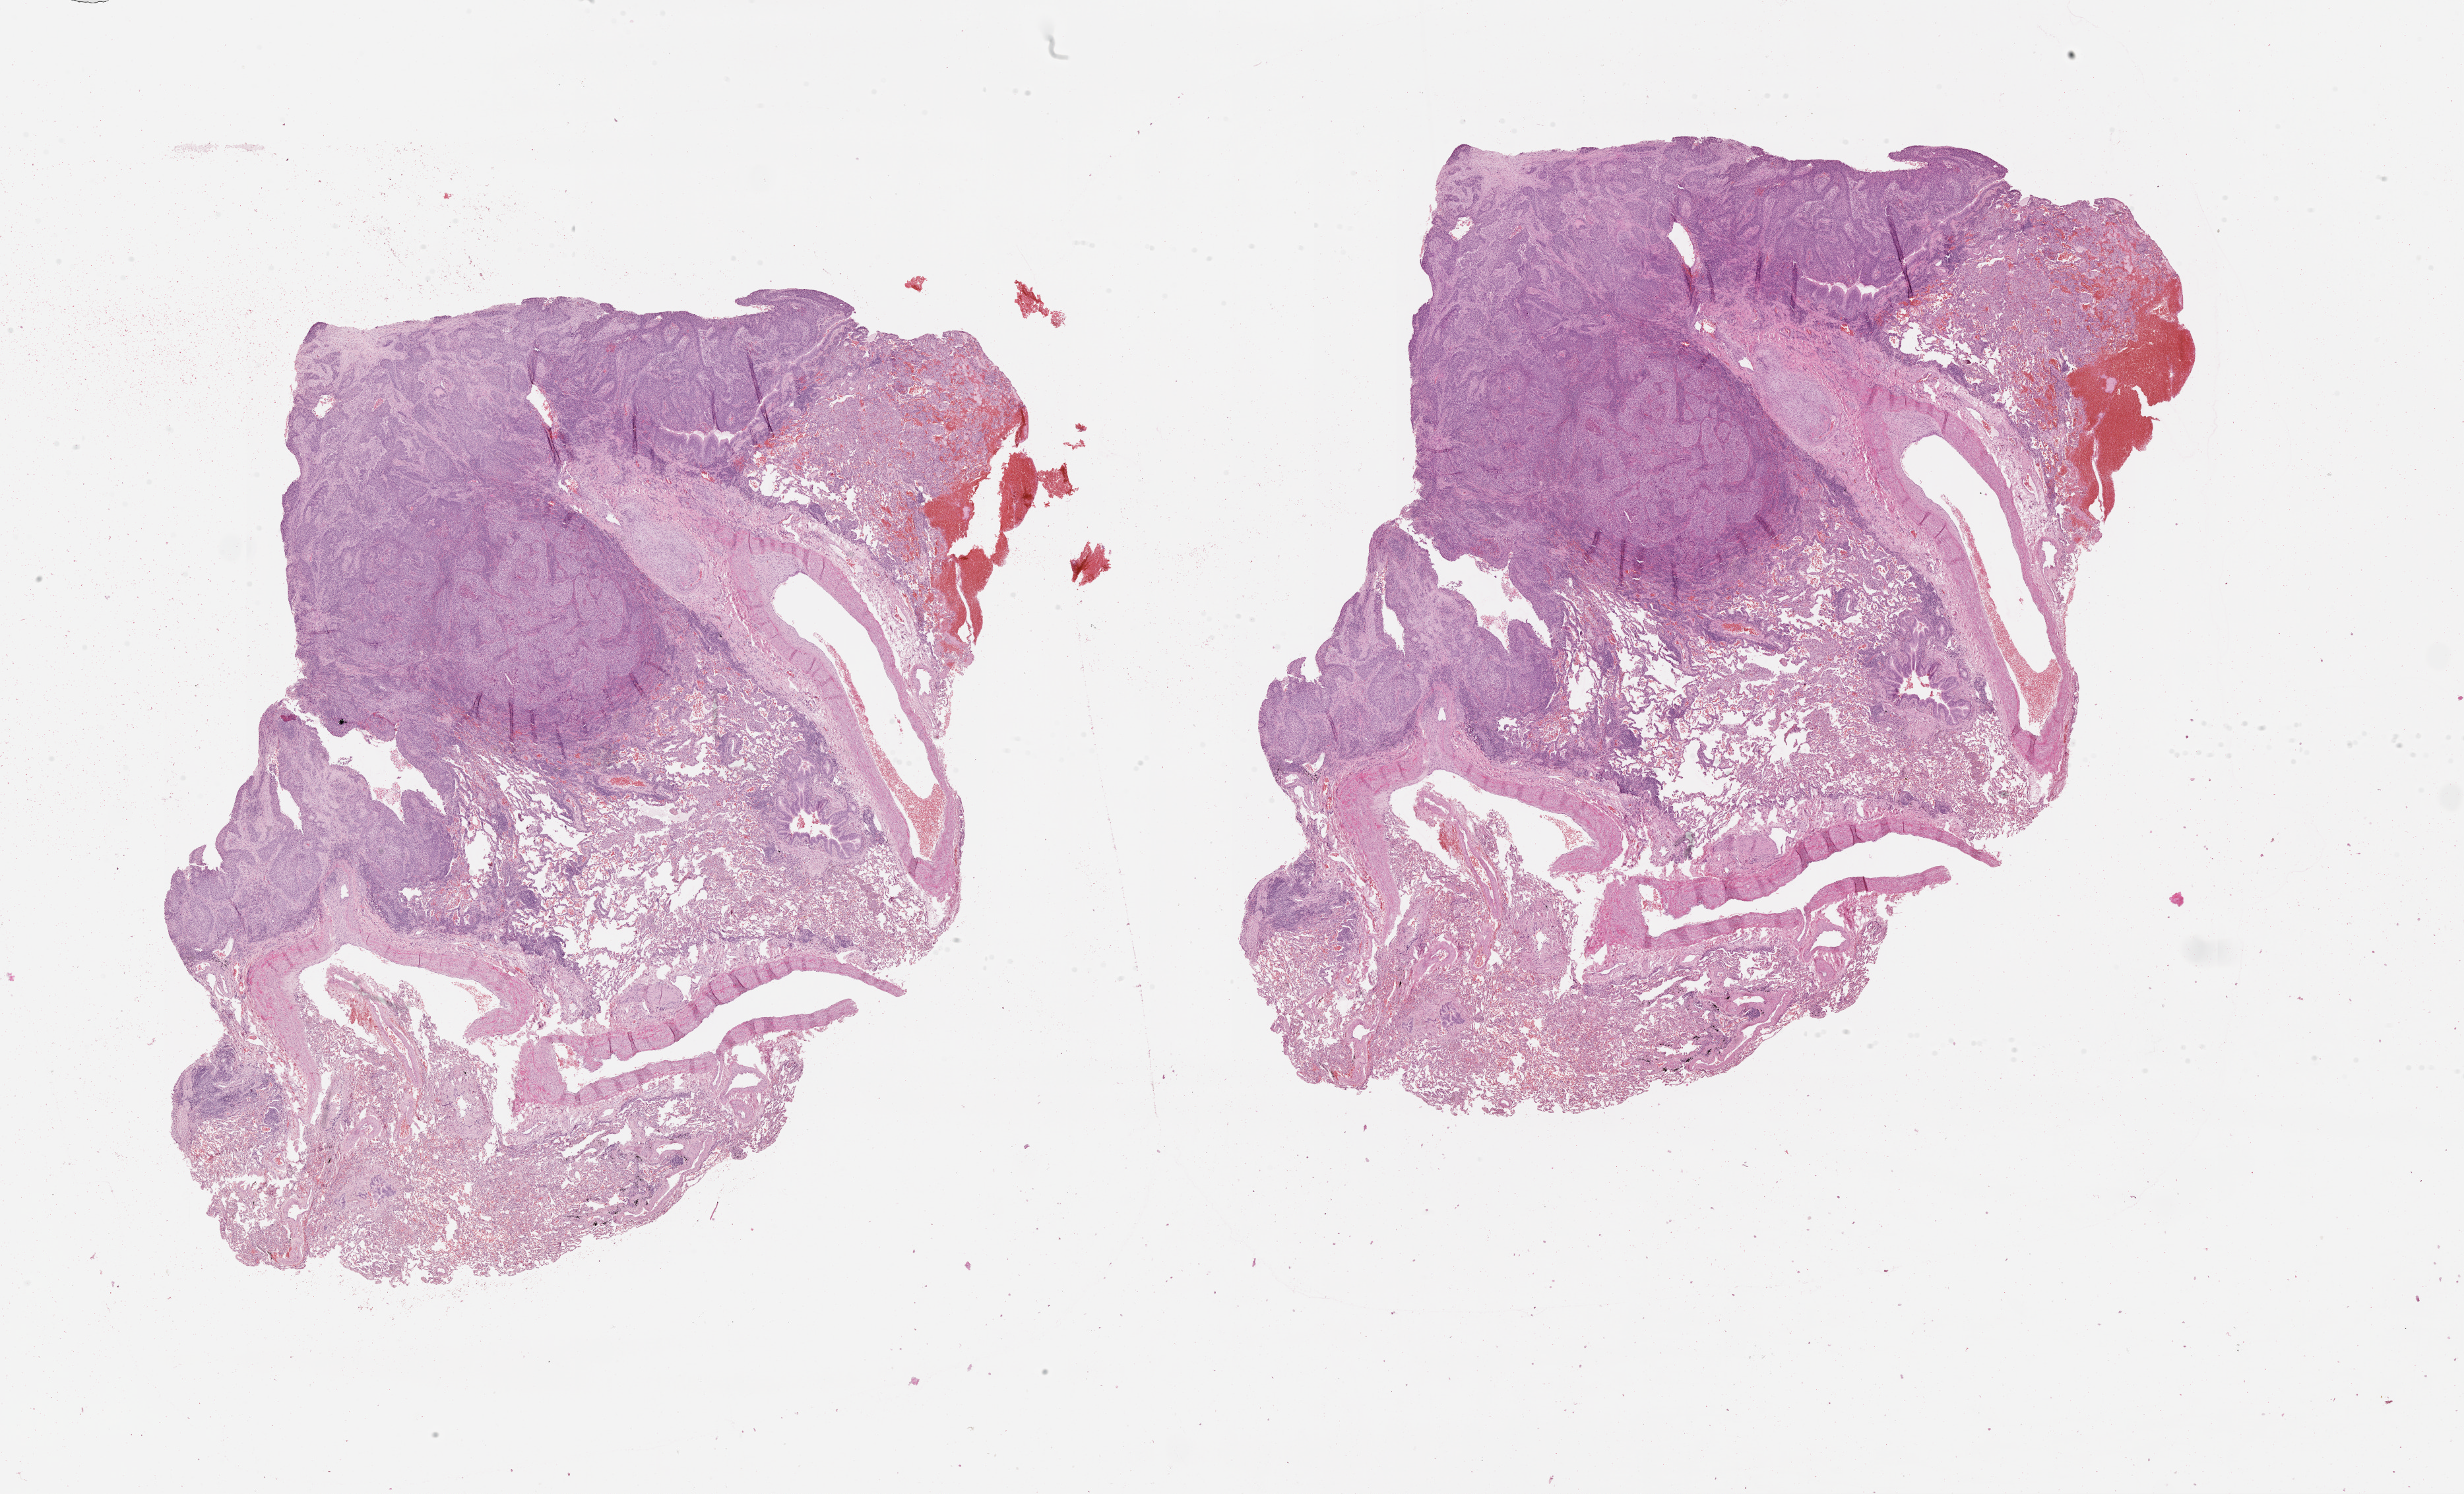
Digitized H&E-stained tissue section (whole slide) — shown as a low-resolution overview of the whole scanned area (about 30.1 x 18.2 mm, slide scanned at 20x); tumour tissue sample, lung. 69-year-old male patient.
Patient diagnosis (cohort enrolment): squamous cell carcinoma (lung).